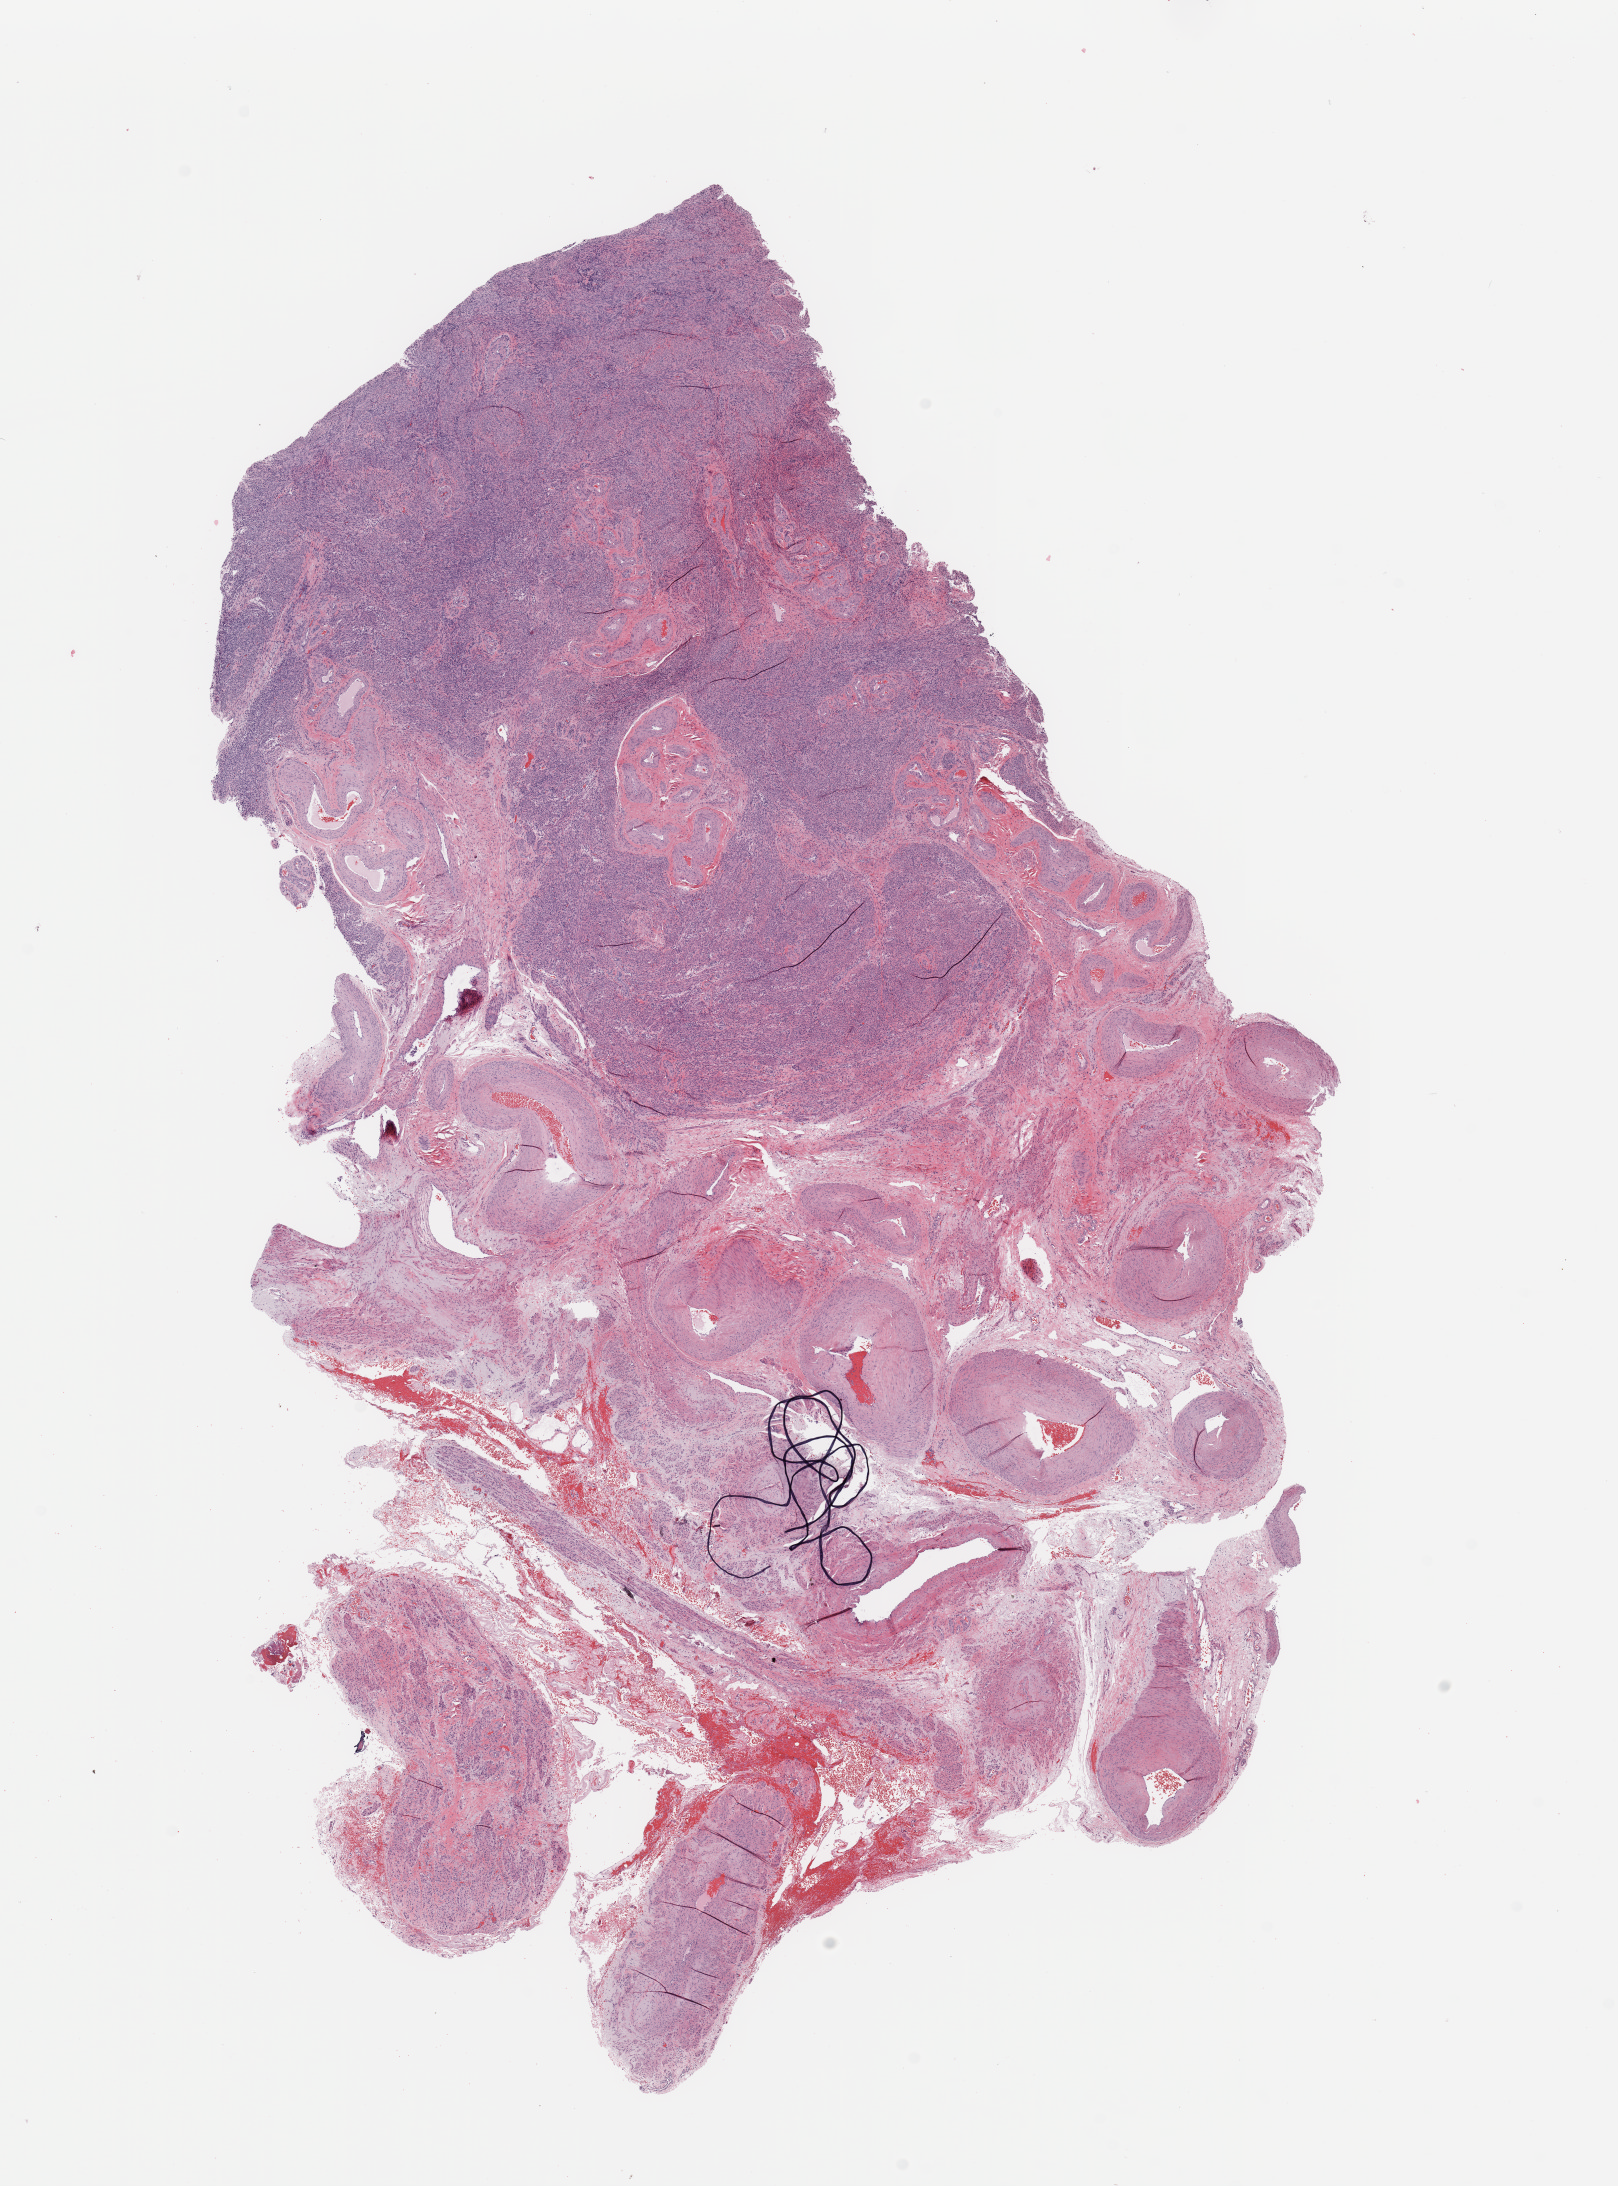
Whole-slide histology image, H&E, whole scanned area (about 12.8 x 17.3 mm, acquisition: 20x scan) shown as a low-resolution overview; normal (non-tumour) tissue sample, uterus. Patient: female, age 62 years.
This section: normal (non-tumour) tissue from the same patient. Patient diagnosis: Endometrioid adenocarcinoma, NOS.